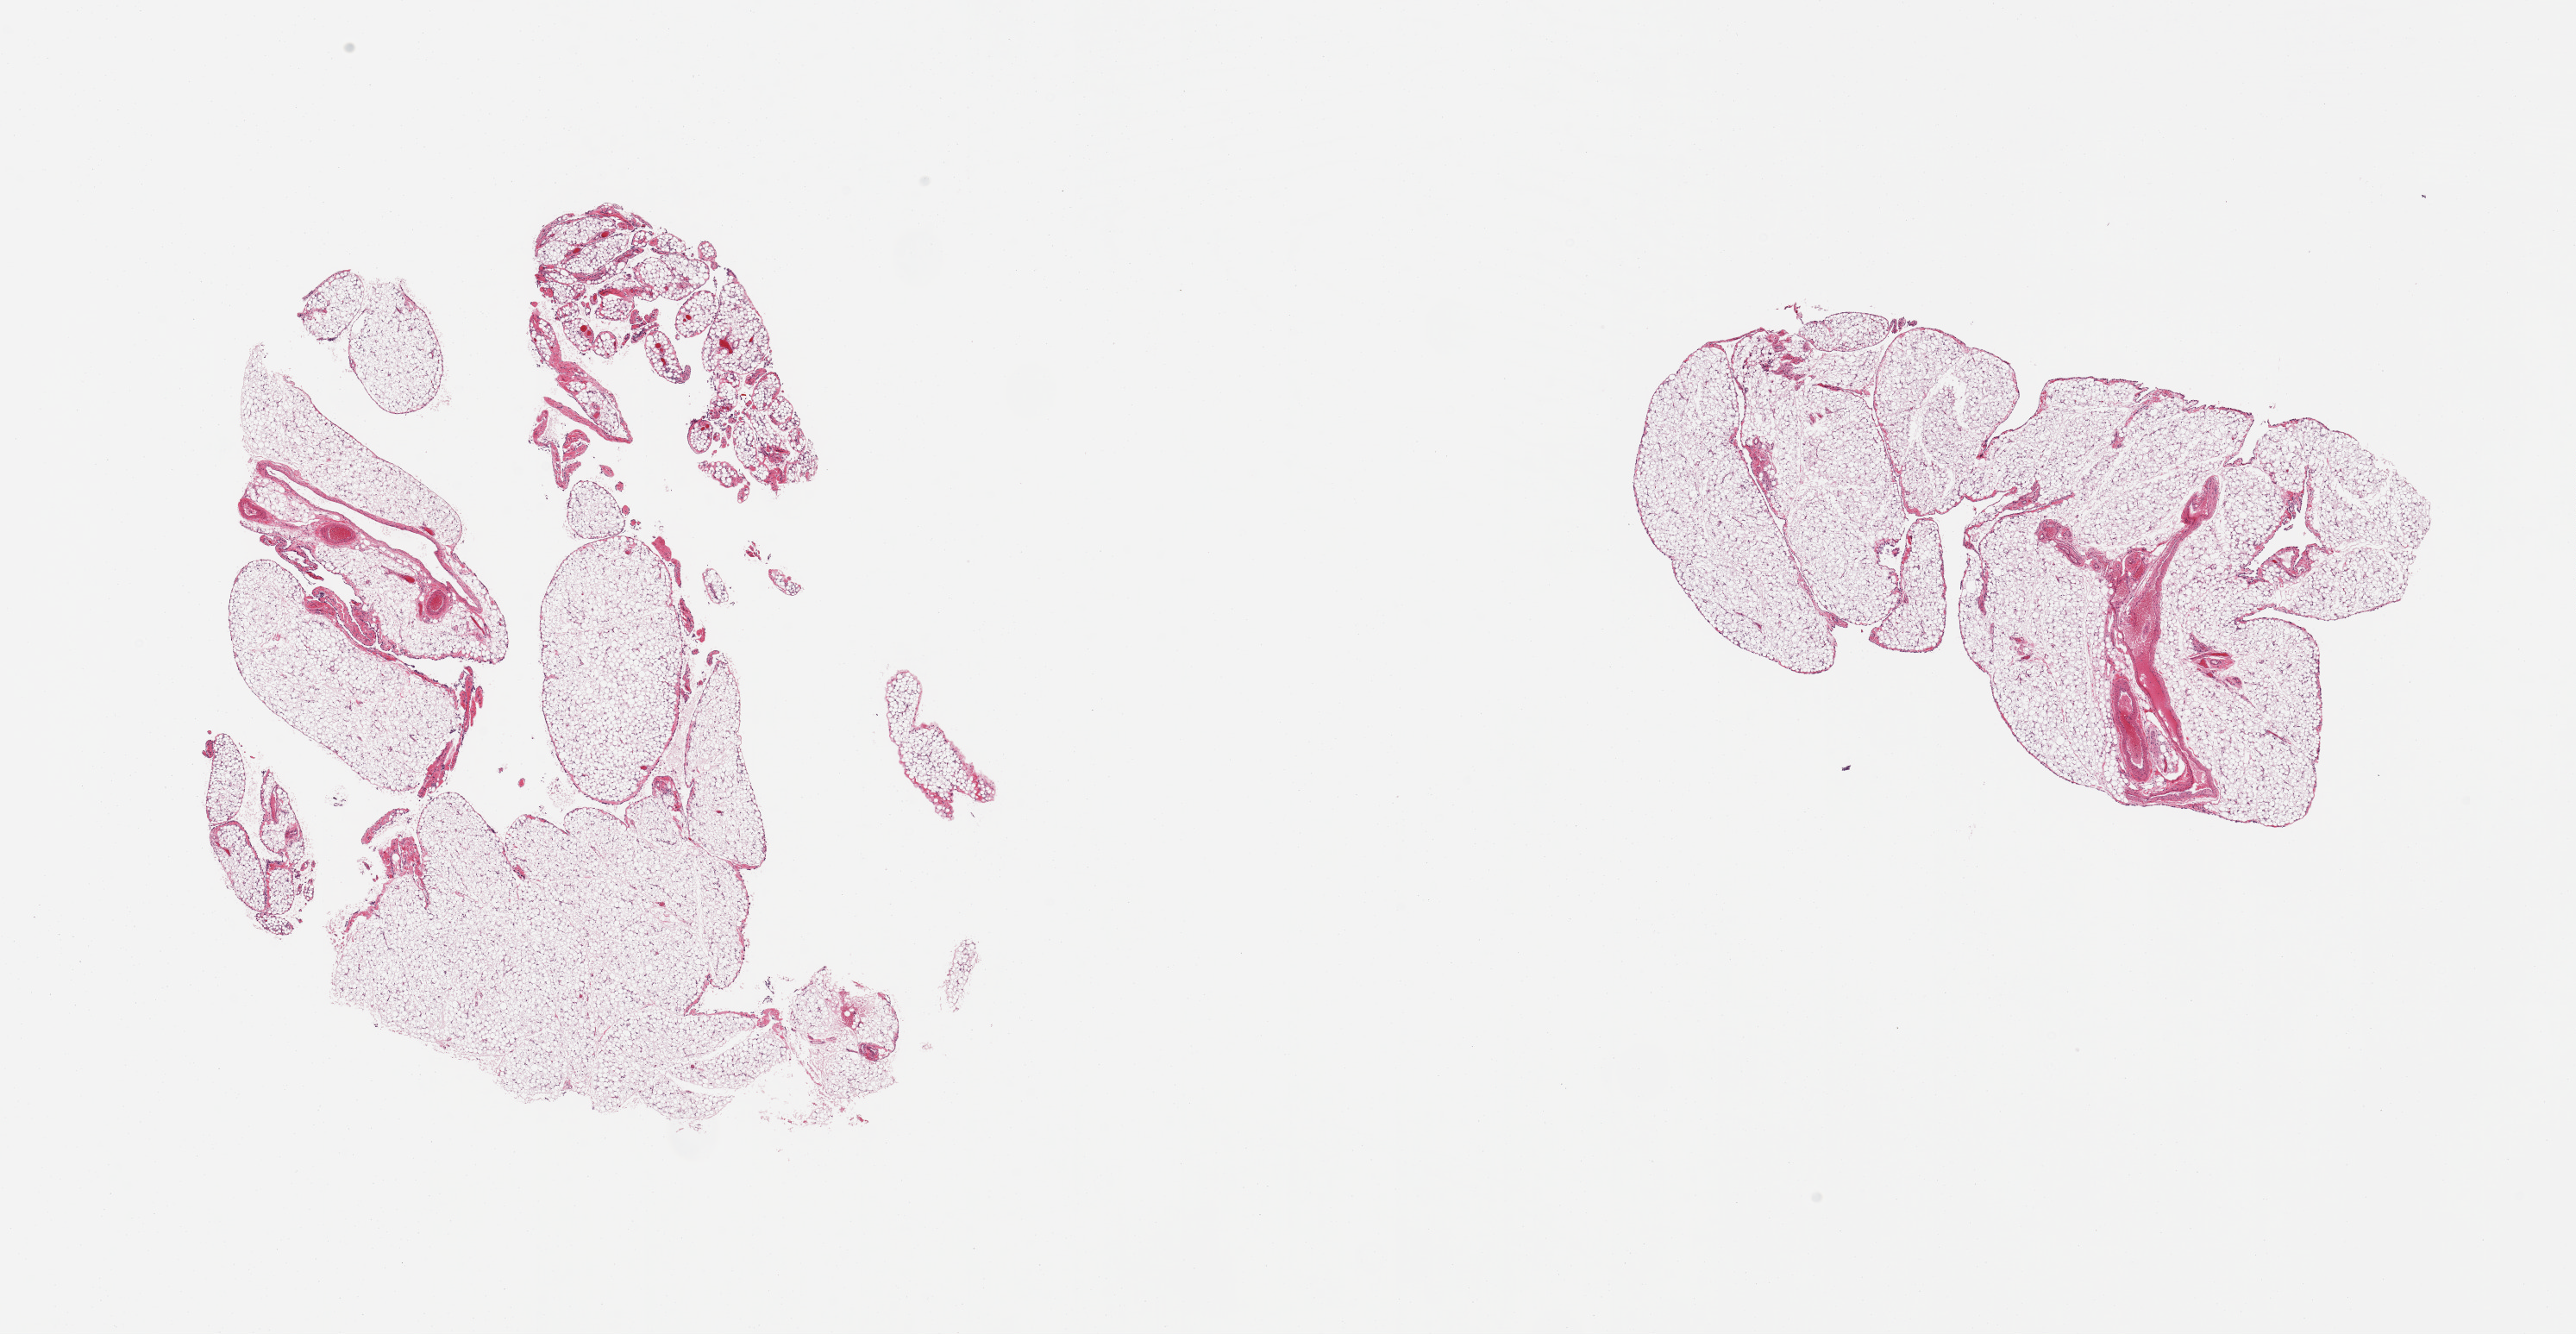
Whole-slide image, hematoxylin and eosin (H&E) stain, a low-resolution overview of the entire scanned area, about 23.6 x 12.2 mm (from a 20x scan); PAXgene-fixed paraffin-embedded (PFPE) section; sampled site (target tissue): omentum; tissue donor sample. Male donor.
Pathologist's review note for this sample: 2 pieces.